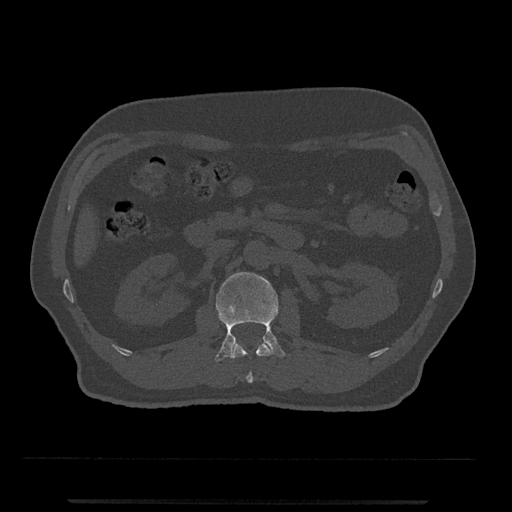
CT including the spine, one axial slice; position 293 of 797 along the scan axis; 120 kVp; bone window (W 1800 / L 400 HU); 0.5 mm slice thickness; 512 × 512 image matrix. Male patient, age 63 years. From the clinical record (not read from this slice): primary cancer: prostate.
Annotated regions visible in this slice (semi-automatically segmented with operator editing):
- L1 vertebra: bounding box <230,343,273,383> (left, top, right, bottom; pixels)
- L2 vertebra: <215,272,285,362>